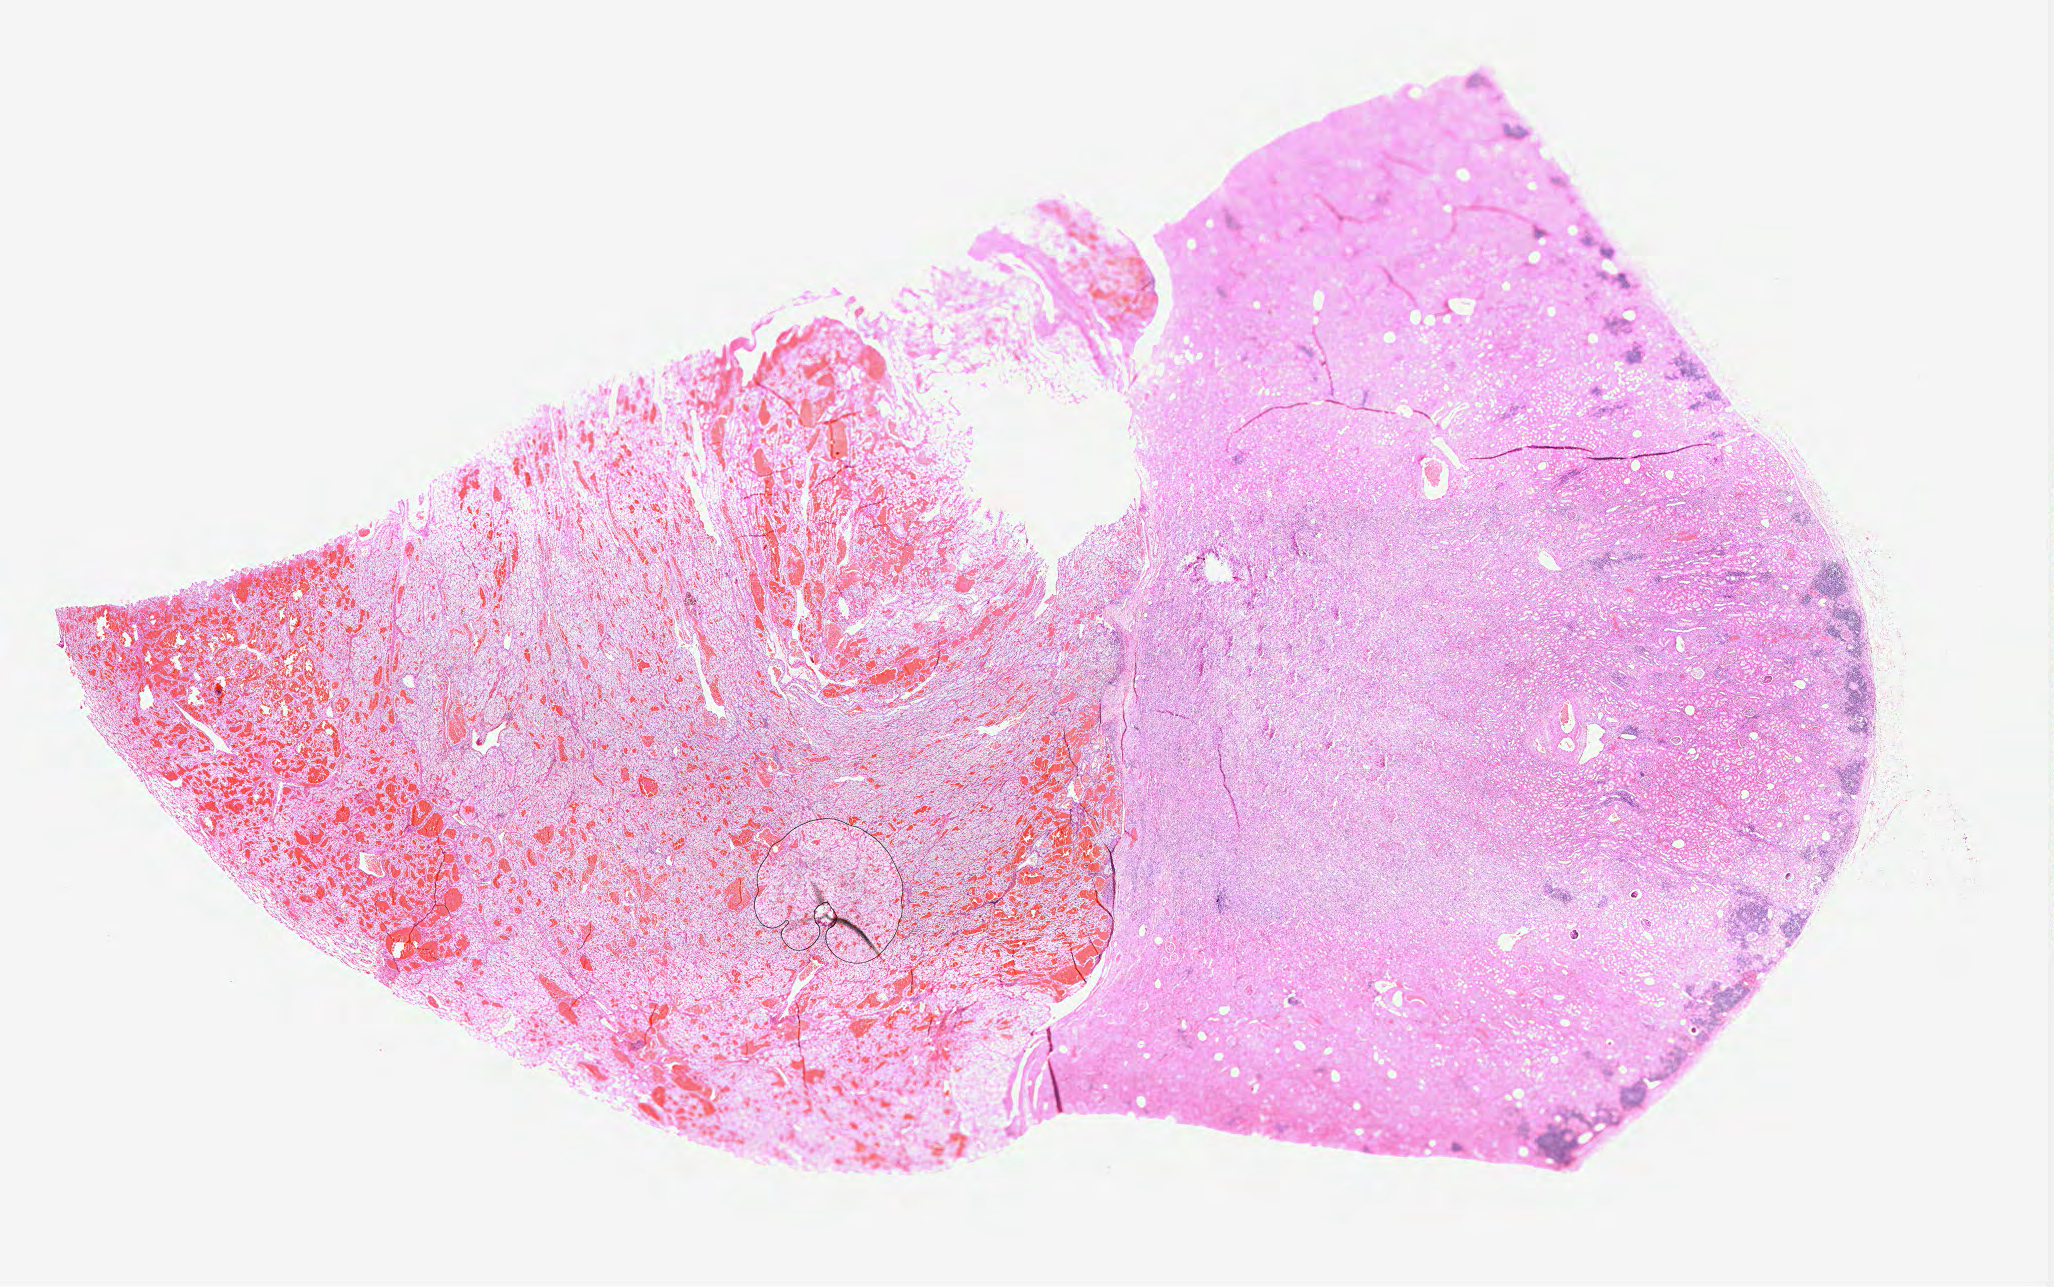
Whole-slide histology image, H&E, a low-resolution overview of the entire scanned area, about 33.1 x 20.8 mm, formalin-fixed paraffin-embedded (FFPE) diagnostic section, primary tumour sample from the kidney. Male, age 63 years at initial diagnosis.
Diagnosis: Clear cell adenocarcinoma, NOS.